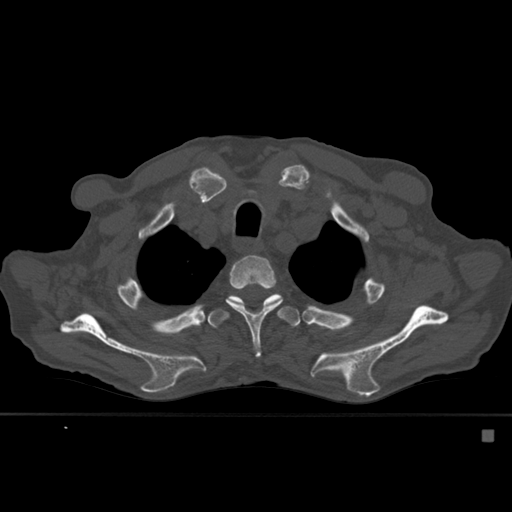
CT including the spine, one axial slice; slice 428 of 527 in the series (ordered by position); bone window (W 1800 / L 400 HU); 512 × 512 image matrix. Male patient, age 78 years. Case-level facts recorded for this patient, not image findings: primary cancer: prostate.
Annotated regions visible in this slice (semi-automatically segmented with operator editing):
- T3 vertebra: box from (x=226, y=255) to (x=282, y=357) px
- T4 vertebra: (x=207, y=286)–(x=301, y=329)